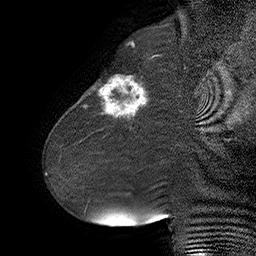
Breast MRI (dynamic contrast-enhanced), one sagittal slice. Position 19 of 55 along the scan axis. Dynamic contrast-enhanced series, time point 2 of 6 at this slice position (early post-contrast). 1.5 T. TE 4.5 ms, TR 32.4 ms. 256 × 256 image matrix, field of view 180 × 180 mm. Female patient. Case-level facts recorded for this patient, not image findings: setting: breast cancer imaged before/during neoadjuvant chemotherapy; receptor status: HER2-positive.
Annotated regions visible in this slice (semi-automatically segmented with operator editing):
- analysis volume of interest (the breast-tissue region the enhancement analysis was run in; not a lesion): bounding box [x1, y1, x2, y2] px = [80, 64, 163, 134]
- tumour enhancement mask (voxels above the 100 % enhancement threshold inside the analysis volume of interest): [83, 76, 147, 117]